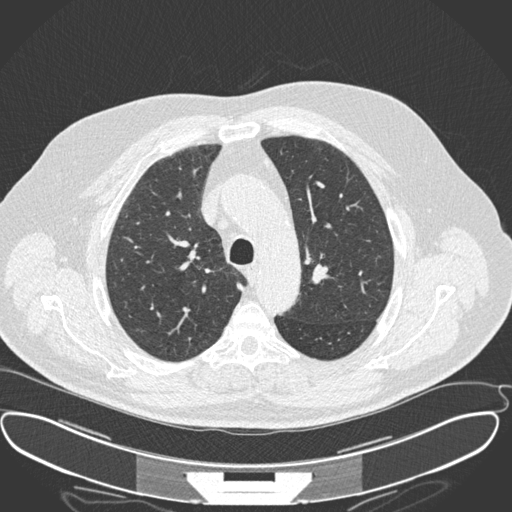
Chest CT (low-dose screening protocol), one axial image. Second annual screen. Lung window (W 1500 / L -600 HU). 2 mm slice thickness. Slice 64 of 220 in the series. 512 × 512 image matrix, field of view 410 × 410 mm. Male participant, aged 64 years at enrolment.
- Expert reader's lesion annotation, bounding box <115,206,137,228> (left, top, right, bottom; pixels).
- Screening reader's record for this exam: no non-calcified nodule ≥4 mm recorded.
- Official screen result: negative screen, no significant abnormalities.
- Participant outcome: lung cancer diagnosed 468 days after this screen — squamous cell carcinoma, NOS, right upper lobe, moderately differentiated (G2), stage IA (AJCC 6th edition), 7 mm at pathology.